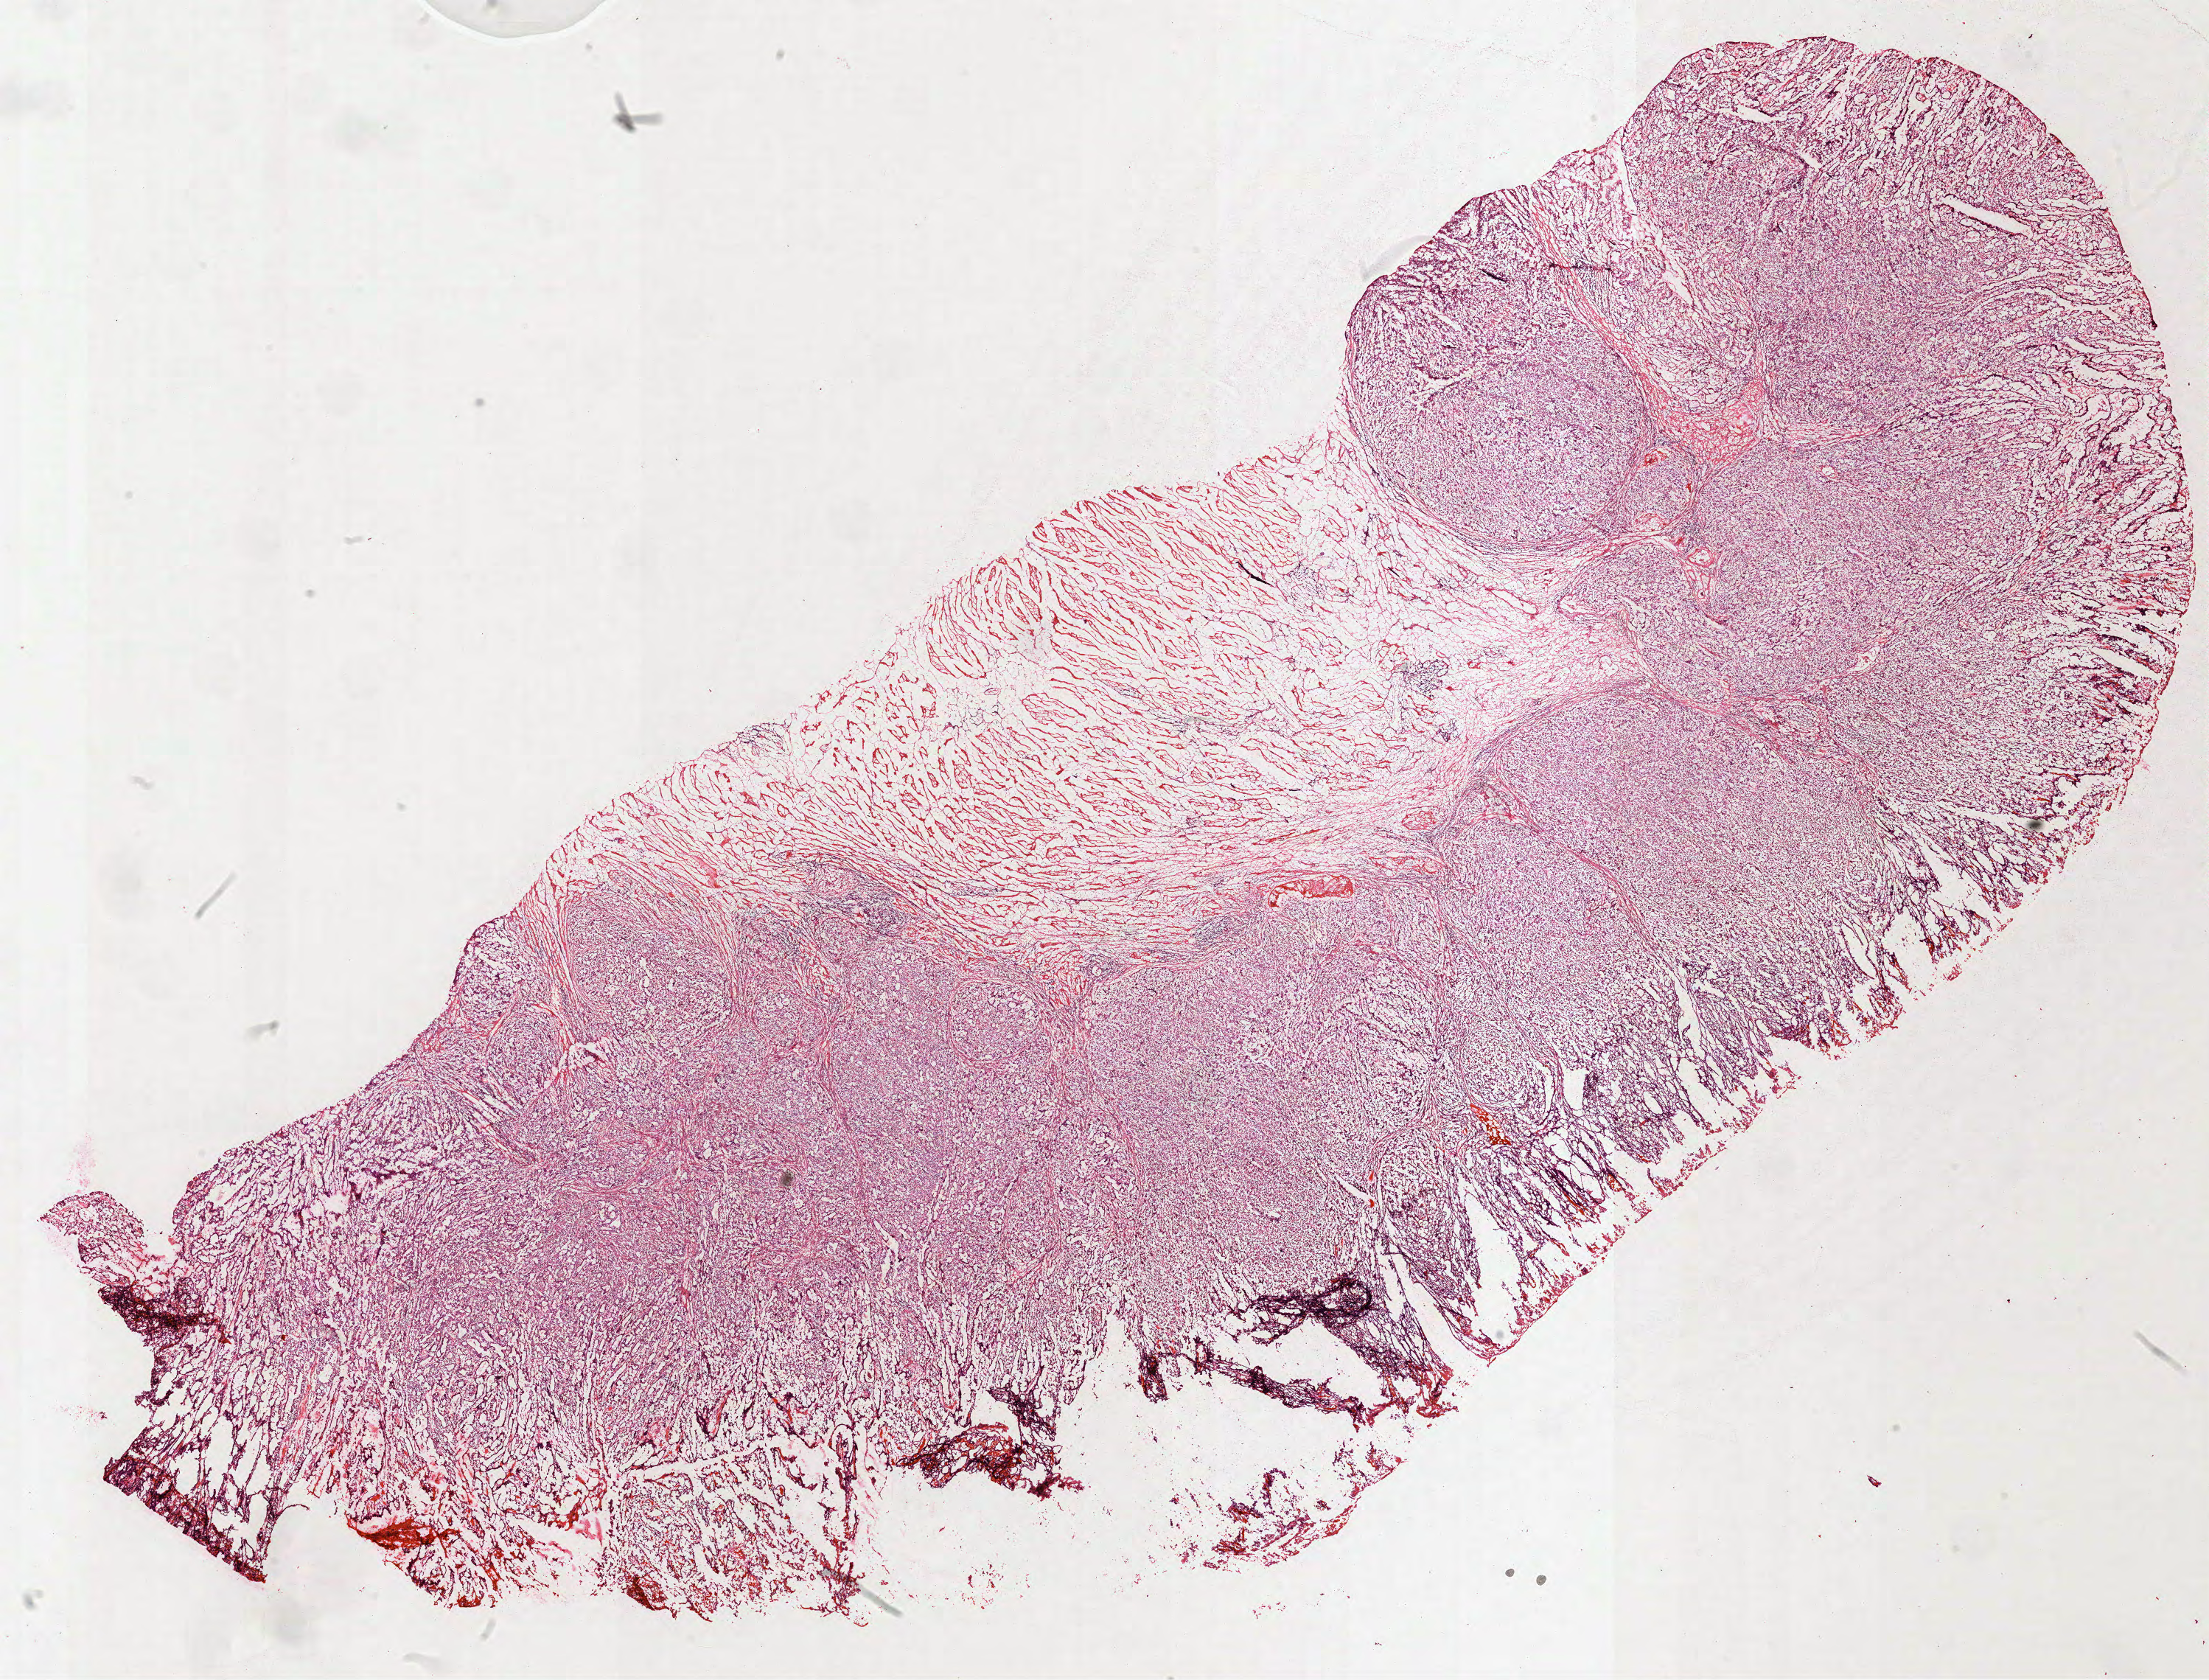
Whole-slide histology image, Hematoxylin and eosin (H&E) stained, whole scanned area (about 24.2 x 18.4 mm, acquisition: 40x scan) shown as a low-resolution overview; frozen section from the top of the tissue portion; primary tumour sample from the stomach. Male patient; age at initial diagnosis 56 years.
Histologic diagnosis: Adenocarcinoma, NOS (fundus of stomach).